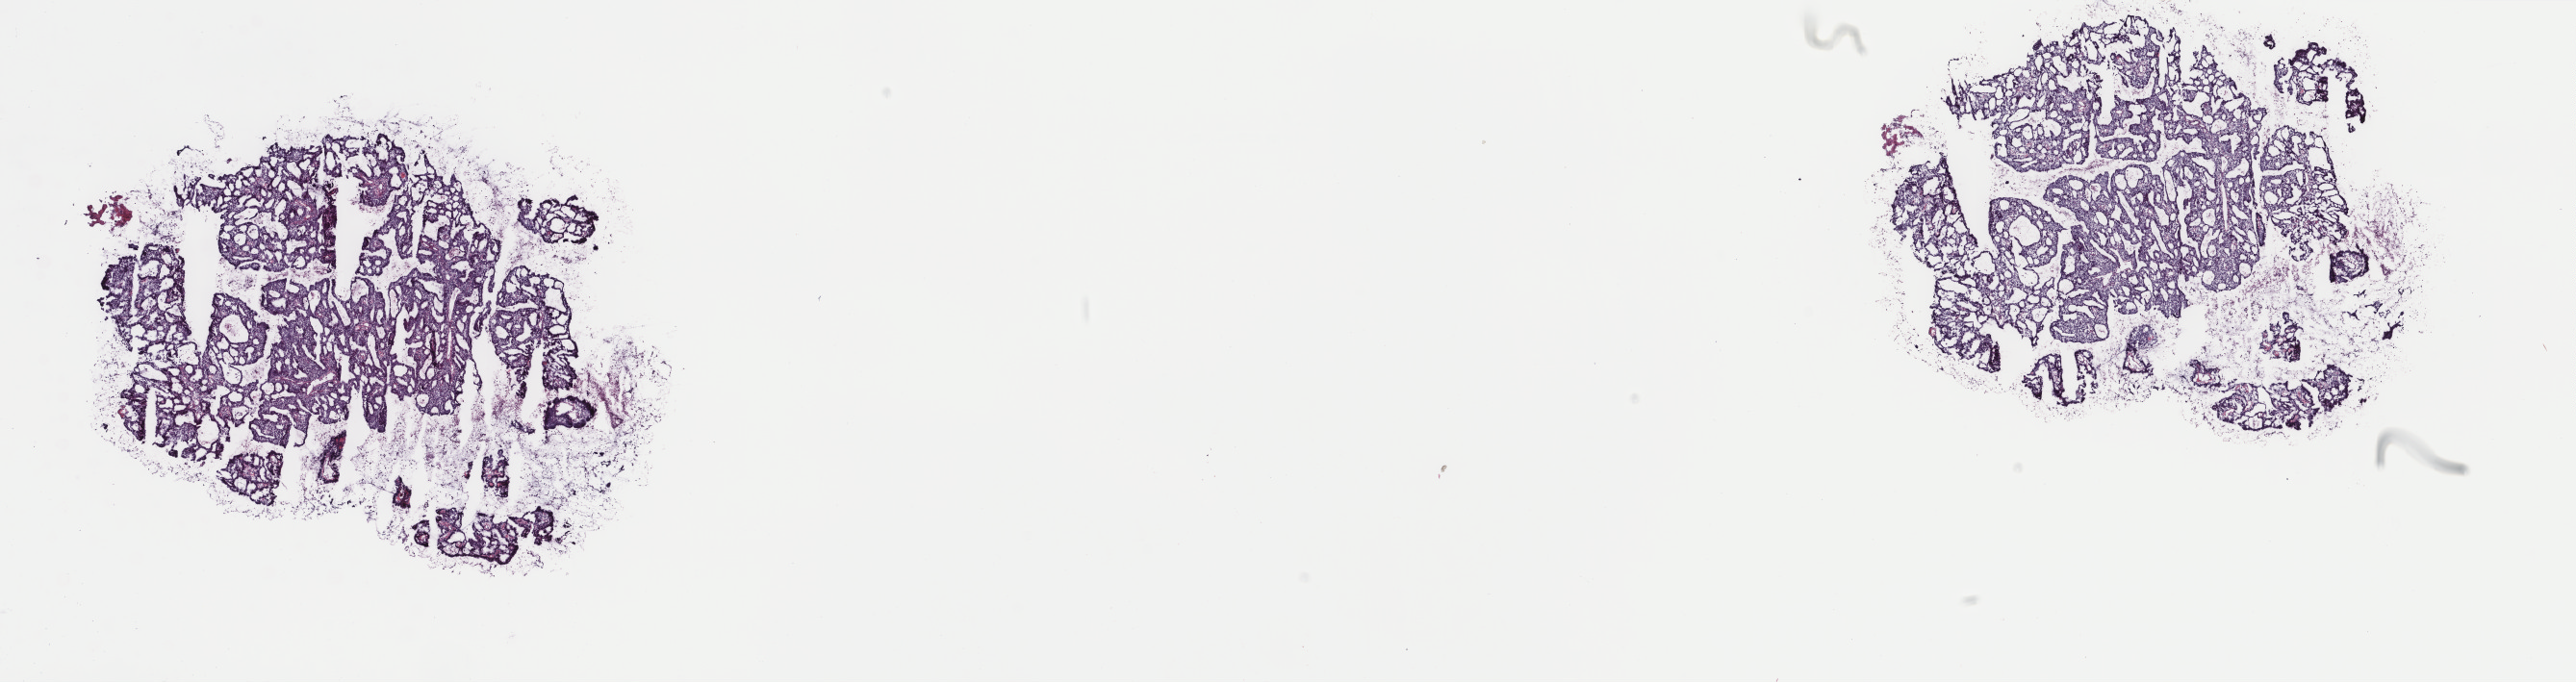
Hematoxylin and eosin (H&E) stained whole-slide image, whole scanned area (about 21.2 x 5.6 mm, slide scanned at 40x) shown as a low-resolution overview. Frozen section from the top of the tissue portion. Cervix, primary tumour sample. Female patient; age at initial diagnosis 42 years. Histologic grade: G1 (well differentiated). Slide review estimates, as recorded: tumour cells 90%, tumour nuclei 80%, normal cells 0%, stromal cells 0%, necrosis 10%. Inflammatory infiltration, as recorded: lymphocyte infiltration 2%, monocyte infiltration 1%, neutrophil infiltration 0%.
Diagnosis: Adenocarcinoma, endocervical type. AJCC pathologic stage: IVB.